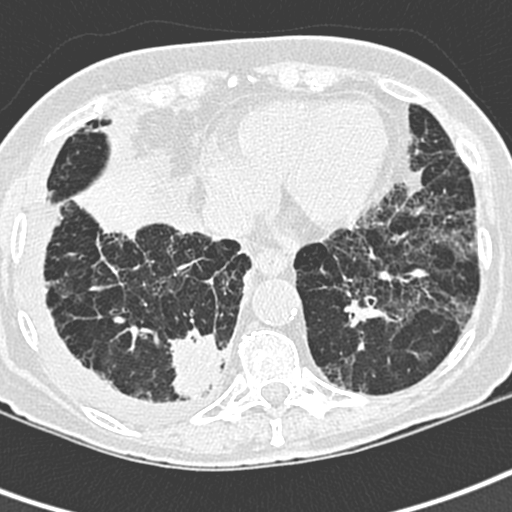
Low-dose screening chest CT, one axial slice. Position 82 of 220 along the scan axis. 120 kVp. Lung window (W 1500 / L -600 HU). 1.3 mm slice thickness. 512 × 512 image matrix, field of view 288 × 288 mm.
Structures marked on this image (manually delineated by an expert):
- lesion 1 (tumor, lower lobe of right lung): bounding box [x1, y1, x2, y2] px = [168, 328, 225, 399]